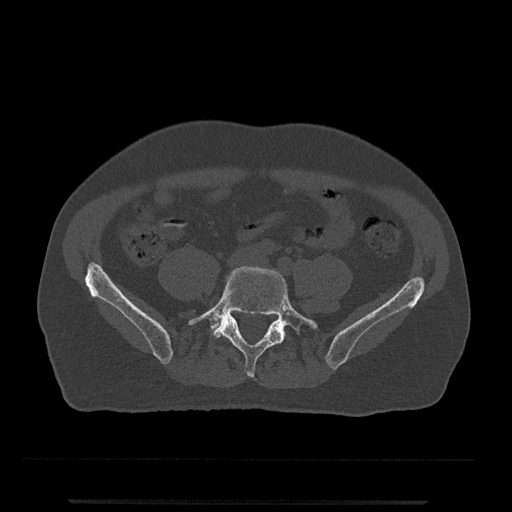
CT including the spine, one axial slice. Position 73 of 797 along the scan axis. Reconstruction kernel Br40s/3. Bone window (W 1800 / L 400 HU). 0.5 mm slice thickness. 512 × 512 image matrix, field of view 419 × 419 mm. Patient: male, 63 years. Case-level facts recorded for this patient, not image findings: primary cancer: prostate.
Structures marked on this image (semi-automatically segmented with operator editing):
- L5 vertebra: bounding box <188,266,318,378> (left, top, right, bottom; pixels)